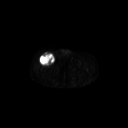
FDG PET of an extremity soft-tissue mass (from a PET/CT study), one axial slice; position 295 of 311 along the scan axis; 3.27 mm slice thickness; 128 × 128 image matrix, field of view 700 × 700 mm. Male patient, age 56 years. From the clinical record (not read from this slice): histological type: pleiomorphic leiomyosarcoma; grade: intermediate; site of the primary tumour: right thigh.
Outlined on this slice (expert contour drawn on MRI and transferred to this co-registered scan by the dataset authors):
- gross tumour volume including surrounding oedema: bounding box <39,52,55,66> (left, top, right, bottom; pixels)
- gross tumour volume (mass): <39,52,55,66>